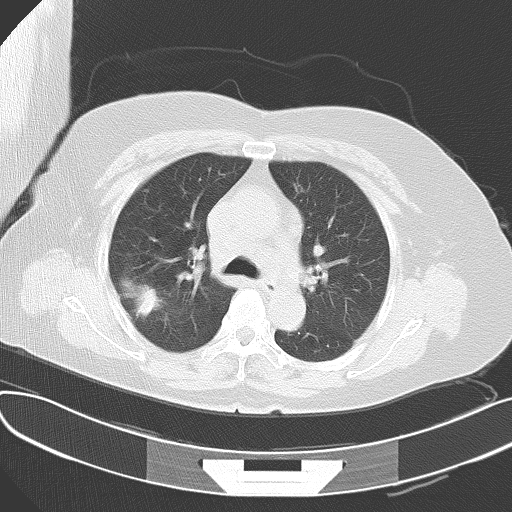
Chest CT, one axial slice. Position 46 of 61 along the scan axis. Reconstruction kernel B70f. Lung window (W 1500 / L -600 HU). 5 mm slice thickness. 512 × 512 image matrix, field of view 367 × 367 mm. Patient: female, 63 years. From the clinical record (not read from this slice): clinical TNM (as recorded): T1c N3 M1a.
Annotated regions visible in this slice (rectangle marked by the reading radiologist):
- lung tumour (recorded histology: adenocarcinoma): bounding box <122,276,162,323> (left, top, right, bottom; pixels)